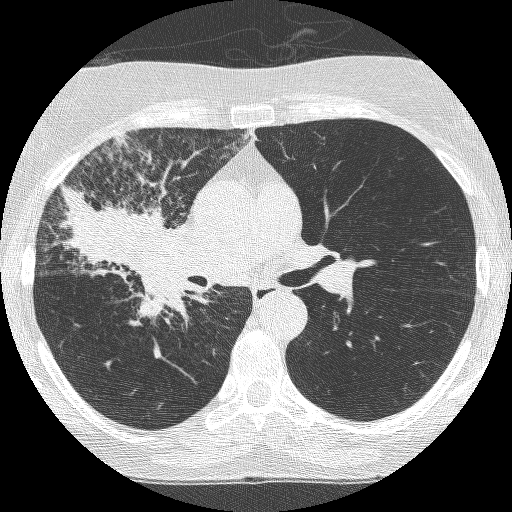
Axial slice from a low-dose chest CT screening exam; third annual screen; lung window (W 1500 / L -600 HU); 1.25 mm slice thickness; lung (sharp) reconstruction kernel (BONE); slice 151 of 253 in the series. Female participant, aged 64 years at enrolment.
Lesion marked by an expert reader, box from (x=71, y=188) to (x=203, y=321) px. The exam's reader record, not a measurement of the box and not confirmed to be the same lesion: non-calcified nodule or mass ≥4 mm, right upper lobe, 49 × 43 mm, spiculated (stellate) margins, soft tissue attenuation, pre-existing on the prior screen: yes; interval growth: yes. Official screen result: positive, other. Lung cancer was diagnosed 7 days after this screen: adenocarcinoma, NOS, right upper lobe, right middle lobe, right hilum, stage IV (AJCC 6th edition), 85 mm at pathology.